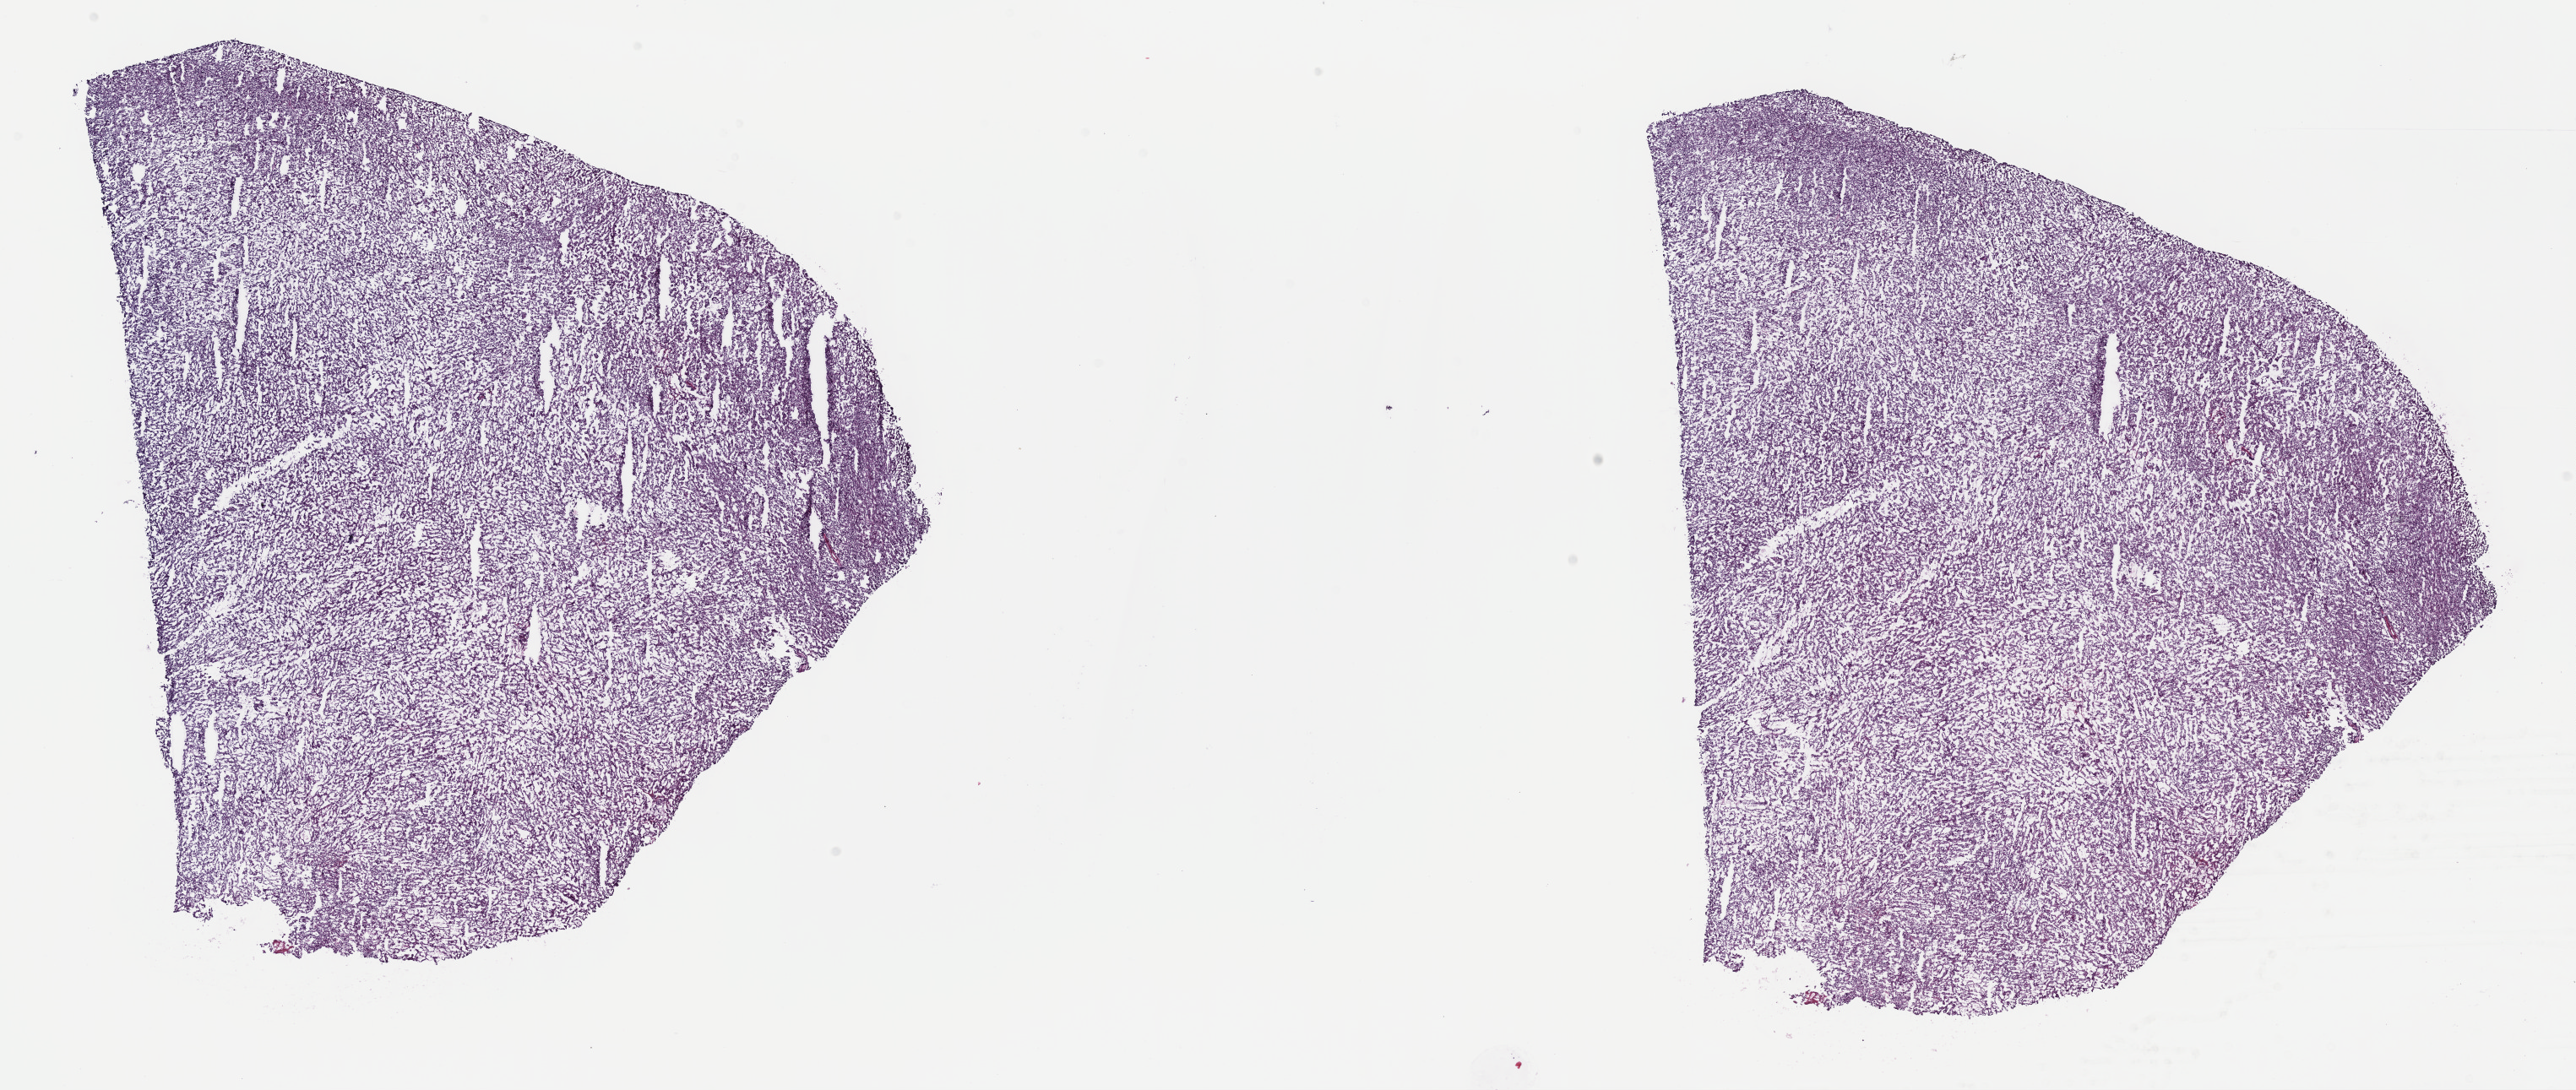
Digitized H&E tissue section (whole slide) — whole scanned area (about 24.7 x 10.4 mm, slide scanned at 40x) shown as a low-resolution overview; frozen section from the top of the tissue portion; sample: primary tumour, kidney. Male patient; age at initial diagnosis 78 years. Pathologist review of this section (percent, as recorded): tumour cells 100%, tumour nuclei 80%, normal cells 0%, stromal cells 0%, necrosis 0%. Inflammatory infiltration, as recorded: lymphocyte infiltration 1%, monocyte infiltration 2%, neutrophil infiltration 0%.
Laterality: right. Diagnosis: Papillary adenocarcinoma, NOS. AJCC pathologic stage: I (6th edition).